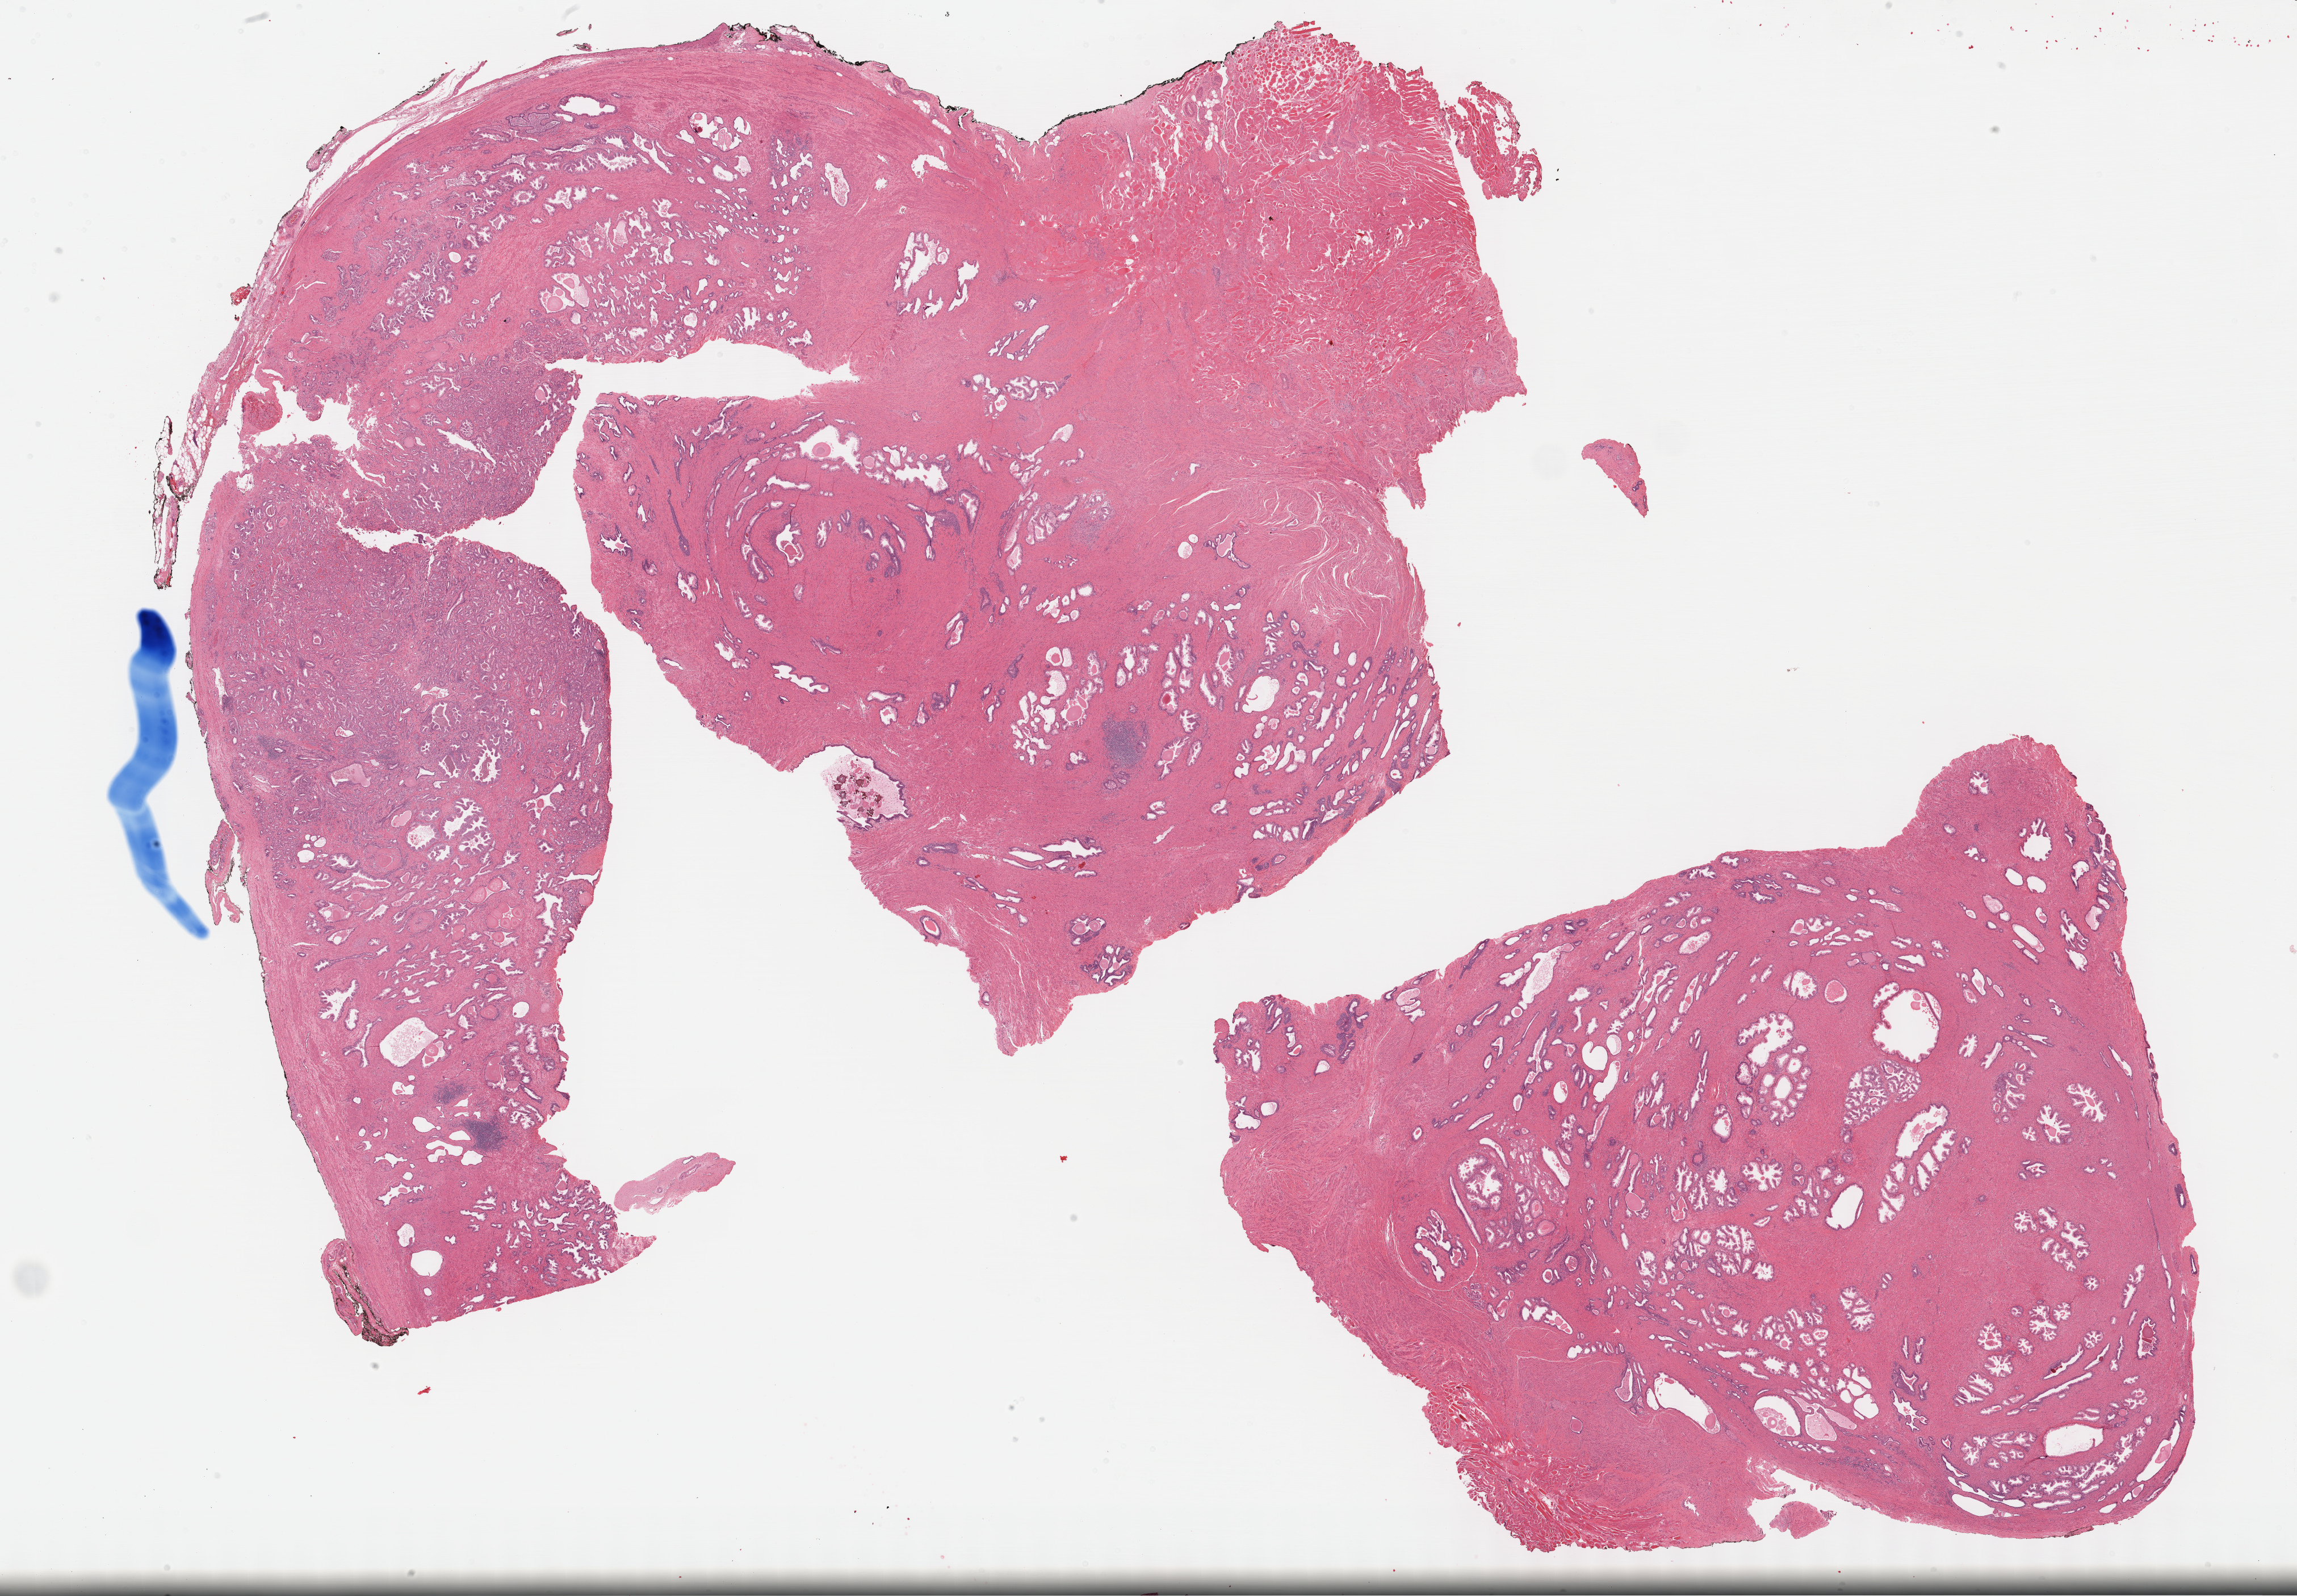
Whole-slide histology image, H&E-stained — low-resolution overview of the scanned area, about 32.7 x 22.7 mm (acquisition: 40x scan). FFPE section. Sample: primary tumour, prostate. Patient: male, age at initial diagnosis 61 years. Gleason score: 7 (3+4).
Laterality: bilateral. Diagnosis: Adenocarcinoma, NOS (prostate gland).